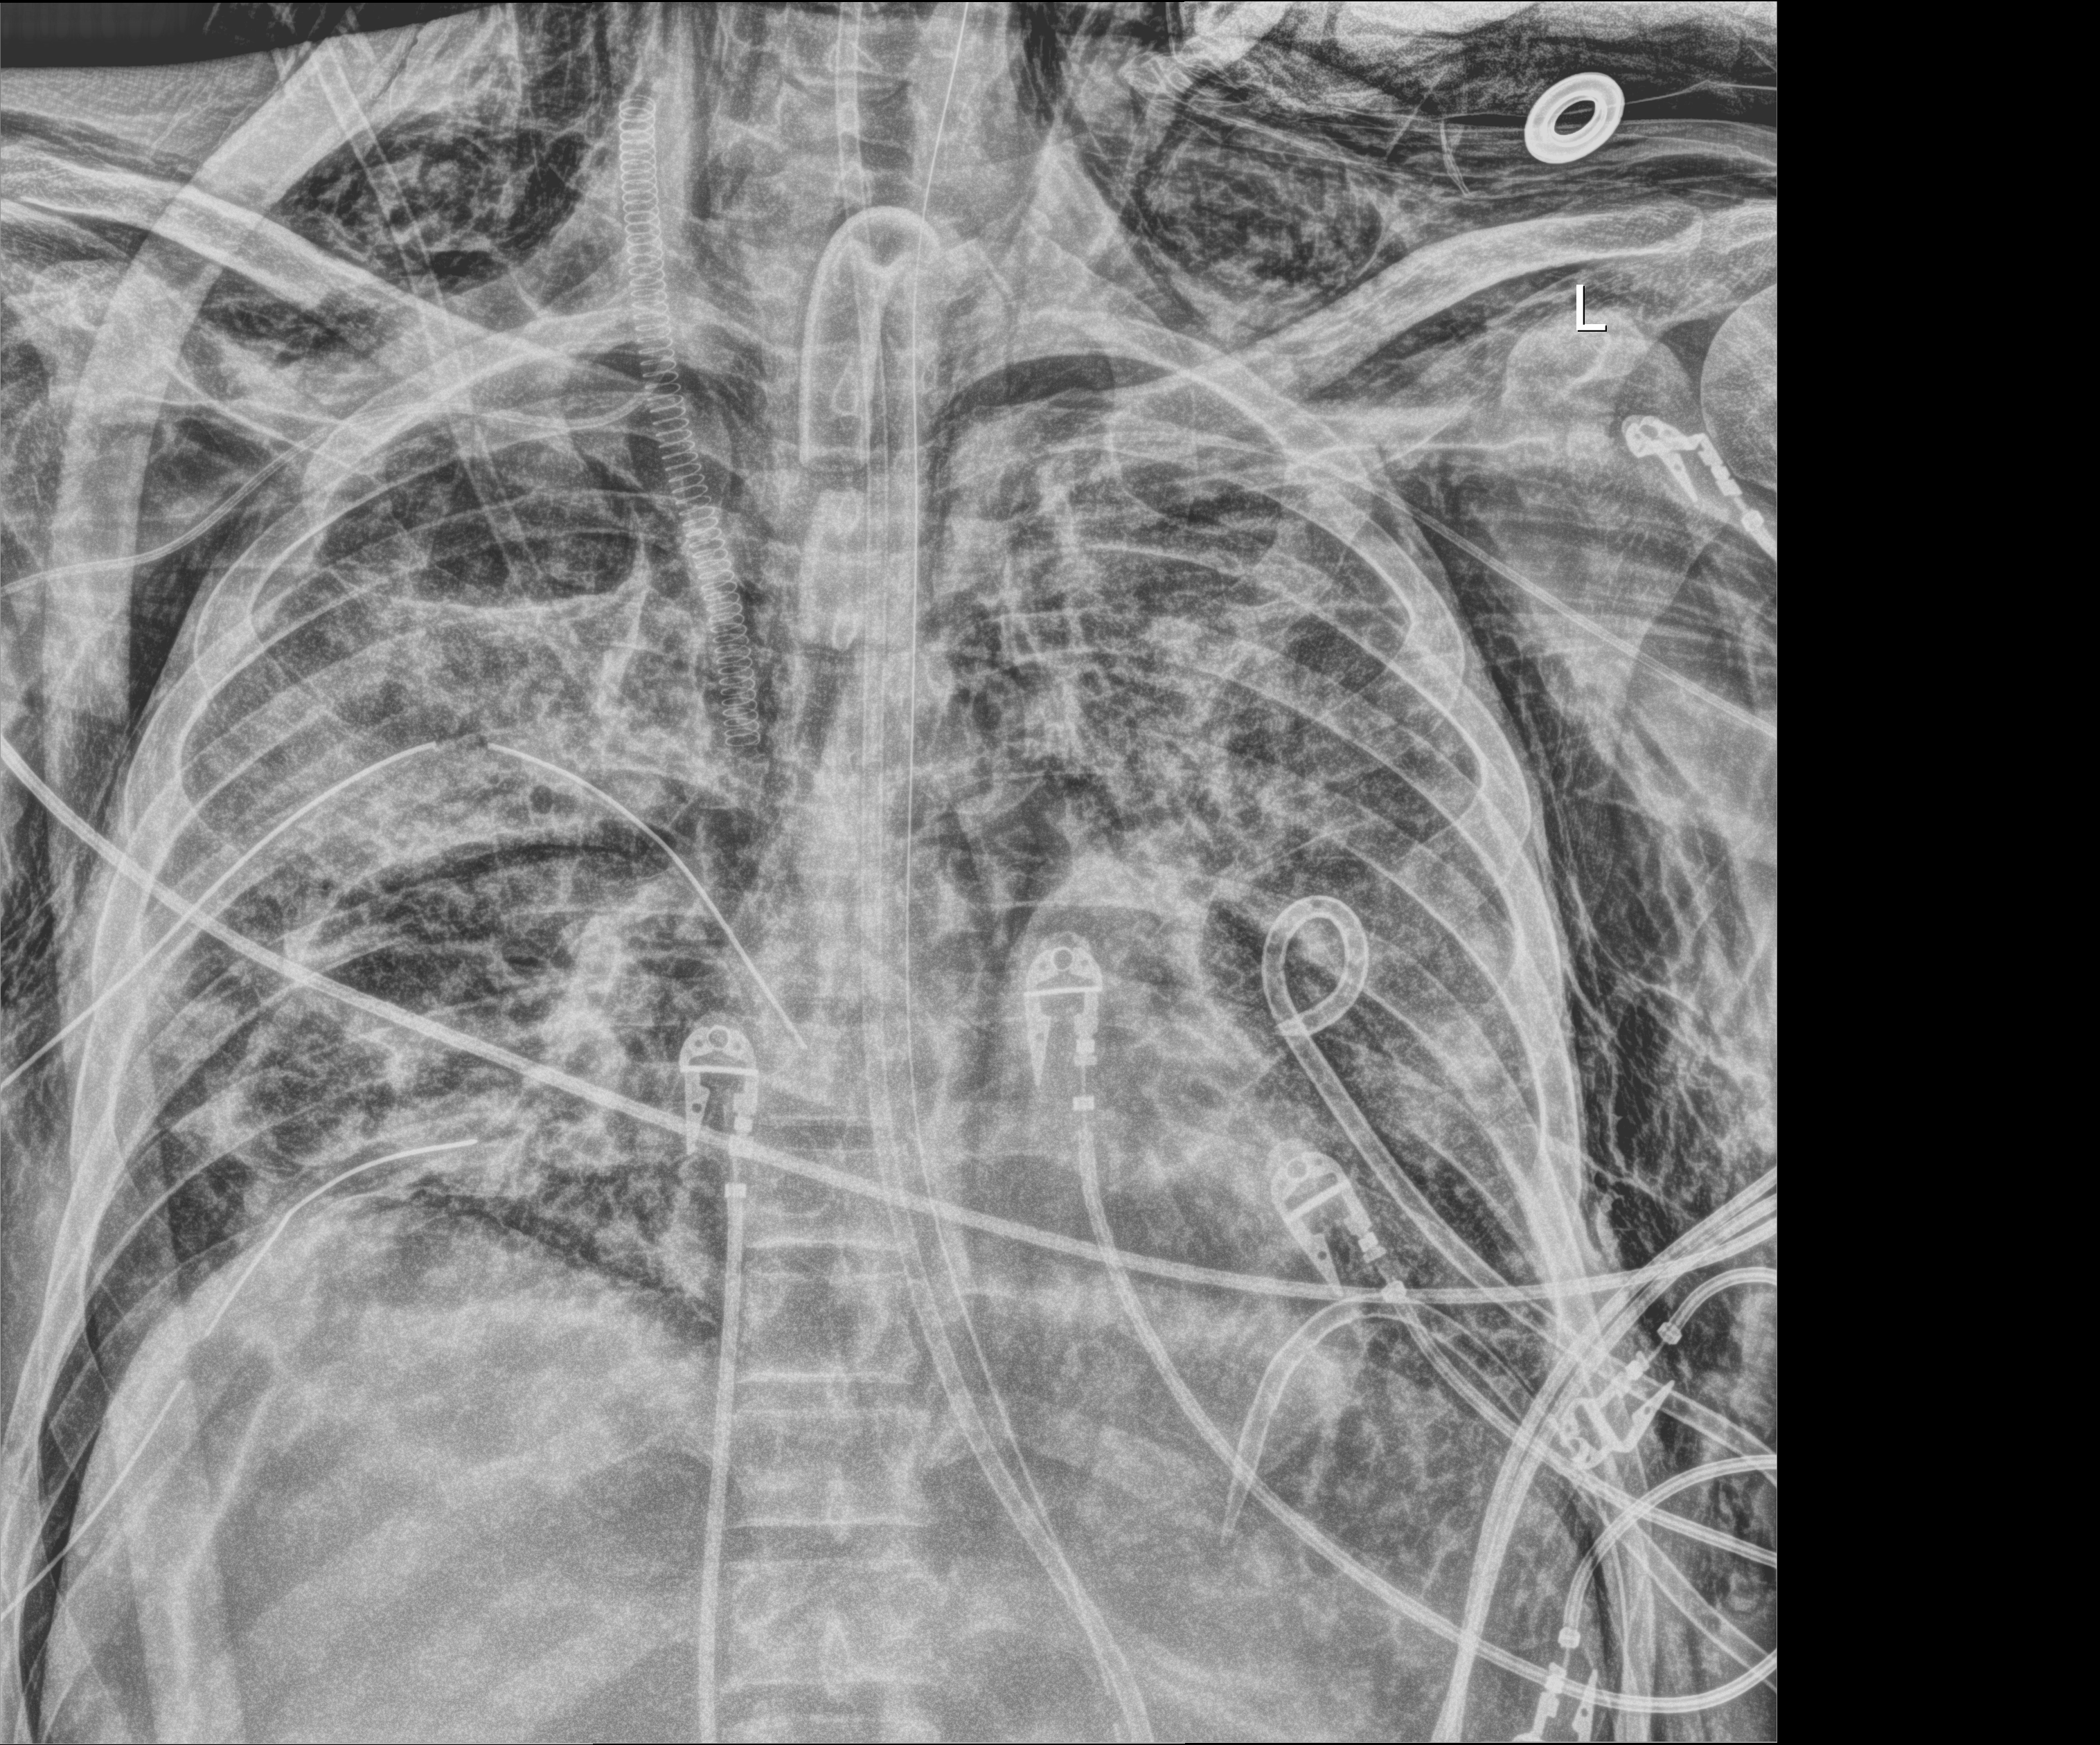
Chest radiograph, anteroposterior (AP) projection. Adult patient hospitalised with COVID-19, age 18–59 years.
Admission-level facts for this patient (not findings on this image; timing relative to this image not recorded): mechanically ventilated during this hospital stay: yes; hypertension (admission record): no; admitted to intensive care during this hospital stay: yes.